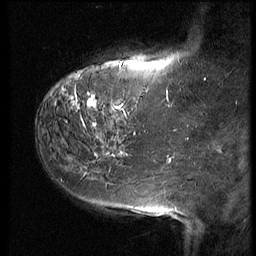
Breast MRI (dynamic contrast-enhanced), one sagittal slice. Slice 16 of 64 in the series (ordered by position). 3 images stored at this slice position (order not interpretable as contrast timing). 1.5 T. TE 4.2 ms, TR 9 ms. 256 × 256 image matrix, field of view 180 × 180 mm. Patient: female, 59 years. From the clinical record (not read from this slice): setting: breast cancer imaged before/during neoadjuvant chemotherapy; receptor status: HER2-positive.
Structures marked on this image (semi-automatic segmentation, software-assisted and operator-edited):
- analysis volume of interest (the breast-tissue region the enhancement analysis was run in; not a lesion): box from (x=54, y=65) to (x=155, y=132) px
- tumour enhancement mask (voxels above the 140 % enhancement threshold inside the analysis volume of interest): (x=62, y=75)–(x=130, y=125)